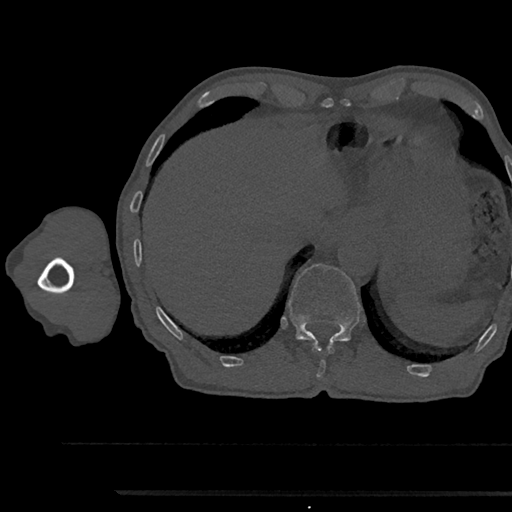
CT including the spine, one axial slice. Position 746 of 797 along the scan axis. Reconstruction kernel Br40s/3. 120 kVp. Bone window (W 1800 / L 400 HU). 0.5 mm slice thickness. 512 × 512 image matrix, field of view 367 × 367 mm. Male patient, age 79 years. From the clinical record (not read from this slice): primary cancer: prostate.
Structures marked on this image (semi-automatic segmentation, software-assisted and operator-edited):
- T11 vertebra: bounding box <313,342,333,377> (left, top, right, bottom; pixels)
- T12 vertebra: <287,264,360,343>